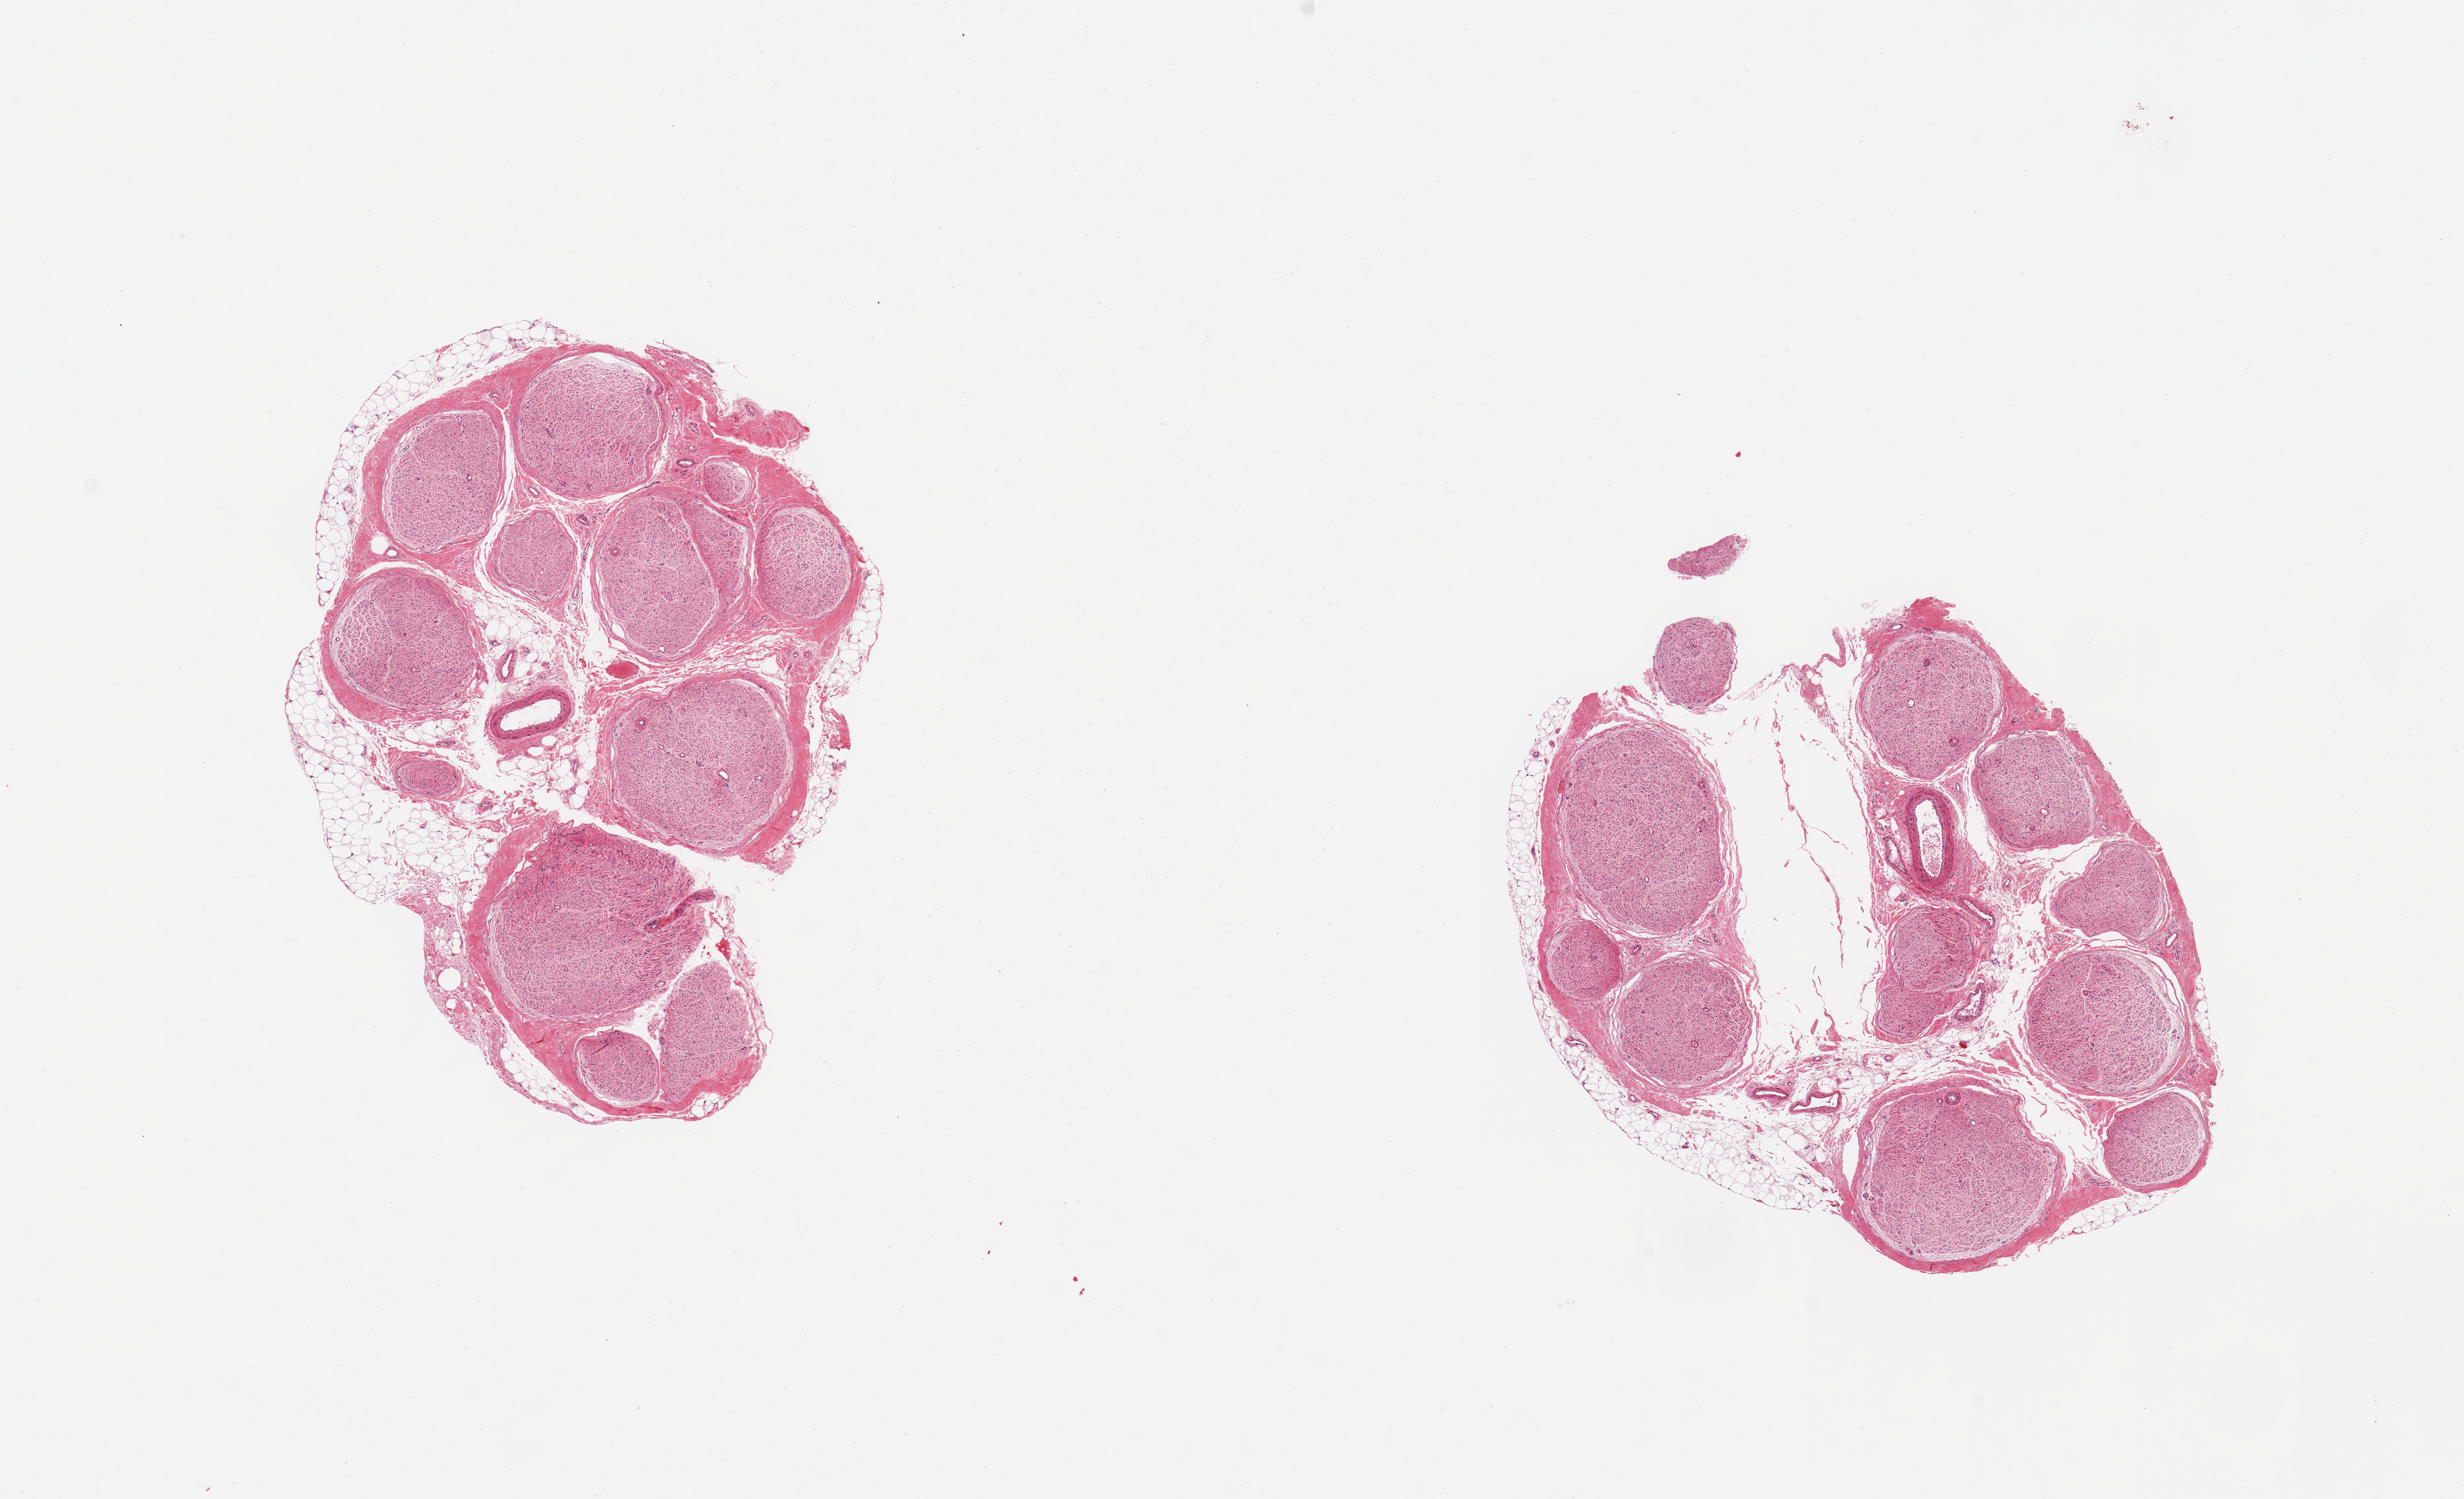
Whole-slide image, haematoxylin and eosin stain, brightfield, low-resolution overview of the scanned area, about 14.8 x 9.0 mm; PAXgene-fixed, paraffin-embedded tissue; target tissue: tibial nerve; donor tissue sample. Donor: male.
Pathologist's review note for this sample: 2 pieces, trace adherent fat.